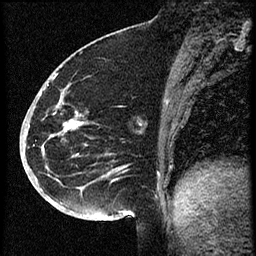
Breast MRI (dynamic contrast-enhanced), one sagittal slice; position 27 of 60 along the scan axis; dynamic contrast-enhanced study with each time point stored as its own series, time point 2 of 3 at this slice position (early post-contrast, ordered by acquisition time); 1.5 T; TE 4.2 ms, TR 18.9 ms; 2 mm slice thickness; 256 × 256 image matrix, field of view 200 × 200 mm. Female patient. From the clinical record (not read from this slice): setting: breast cancer imaged before/during neoadjuvant chemotherapy; receptor status: HR-positive, HER2-negative.
Outlined on this slice (semi-automatically segmented with operator editing):
- analysis volume of interest (the breast-tissue region the enhancement analysis was run in; not a lesion): bounding box (x1, y1, x2, y2) in pixels: (30, 87, 103, 173)
- tumour enhancement mask (voxels above the 100 % enhancement threshold inside the analysis volume of interest): (65, 121, 81, 129)